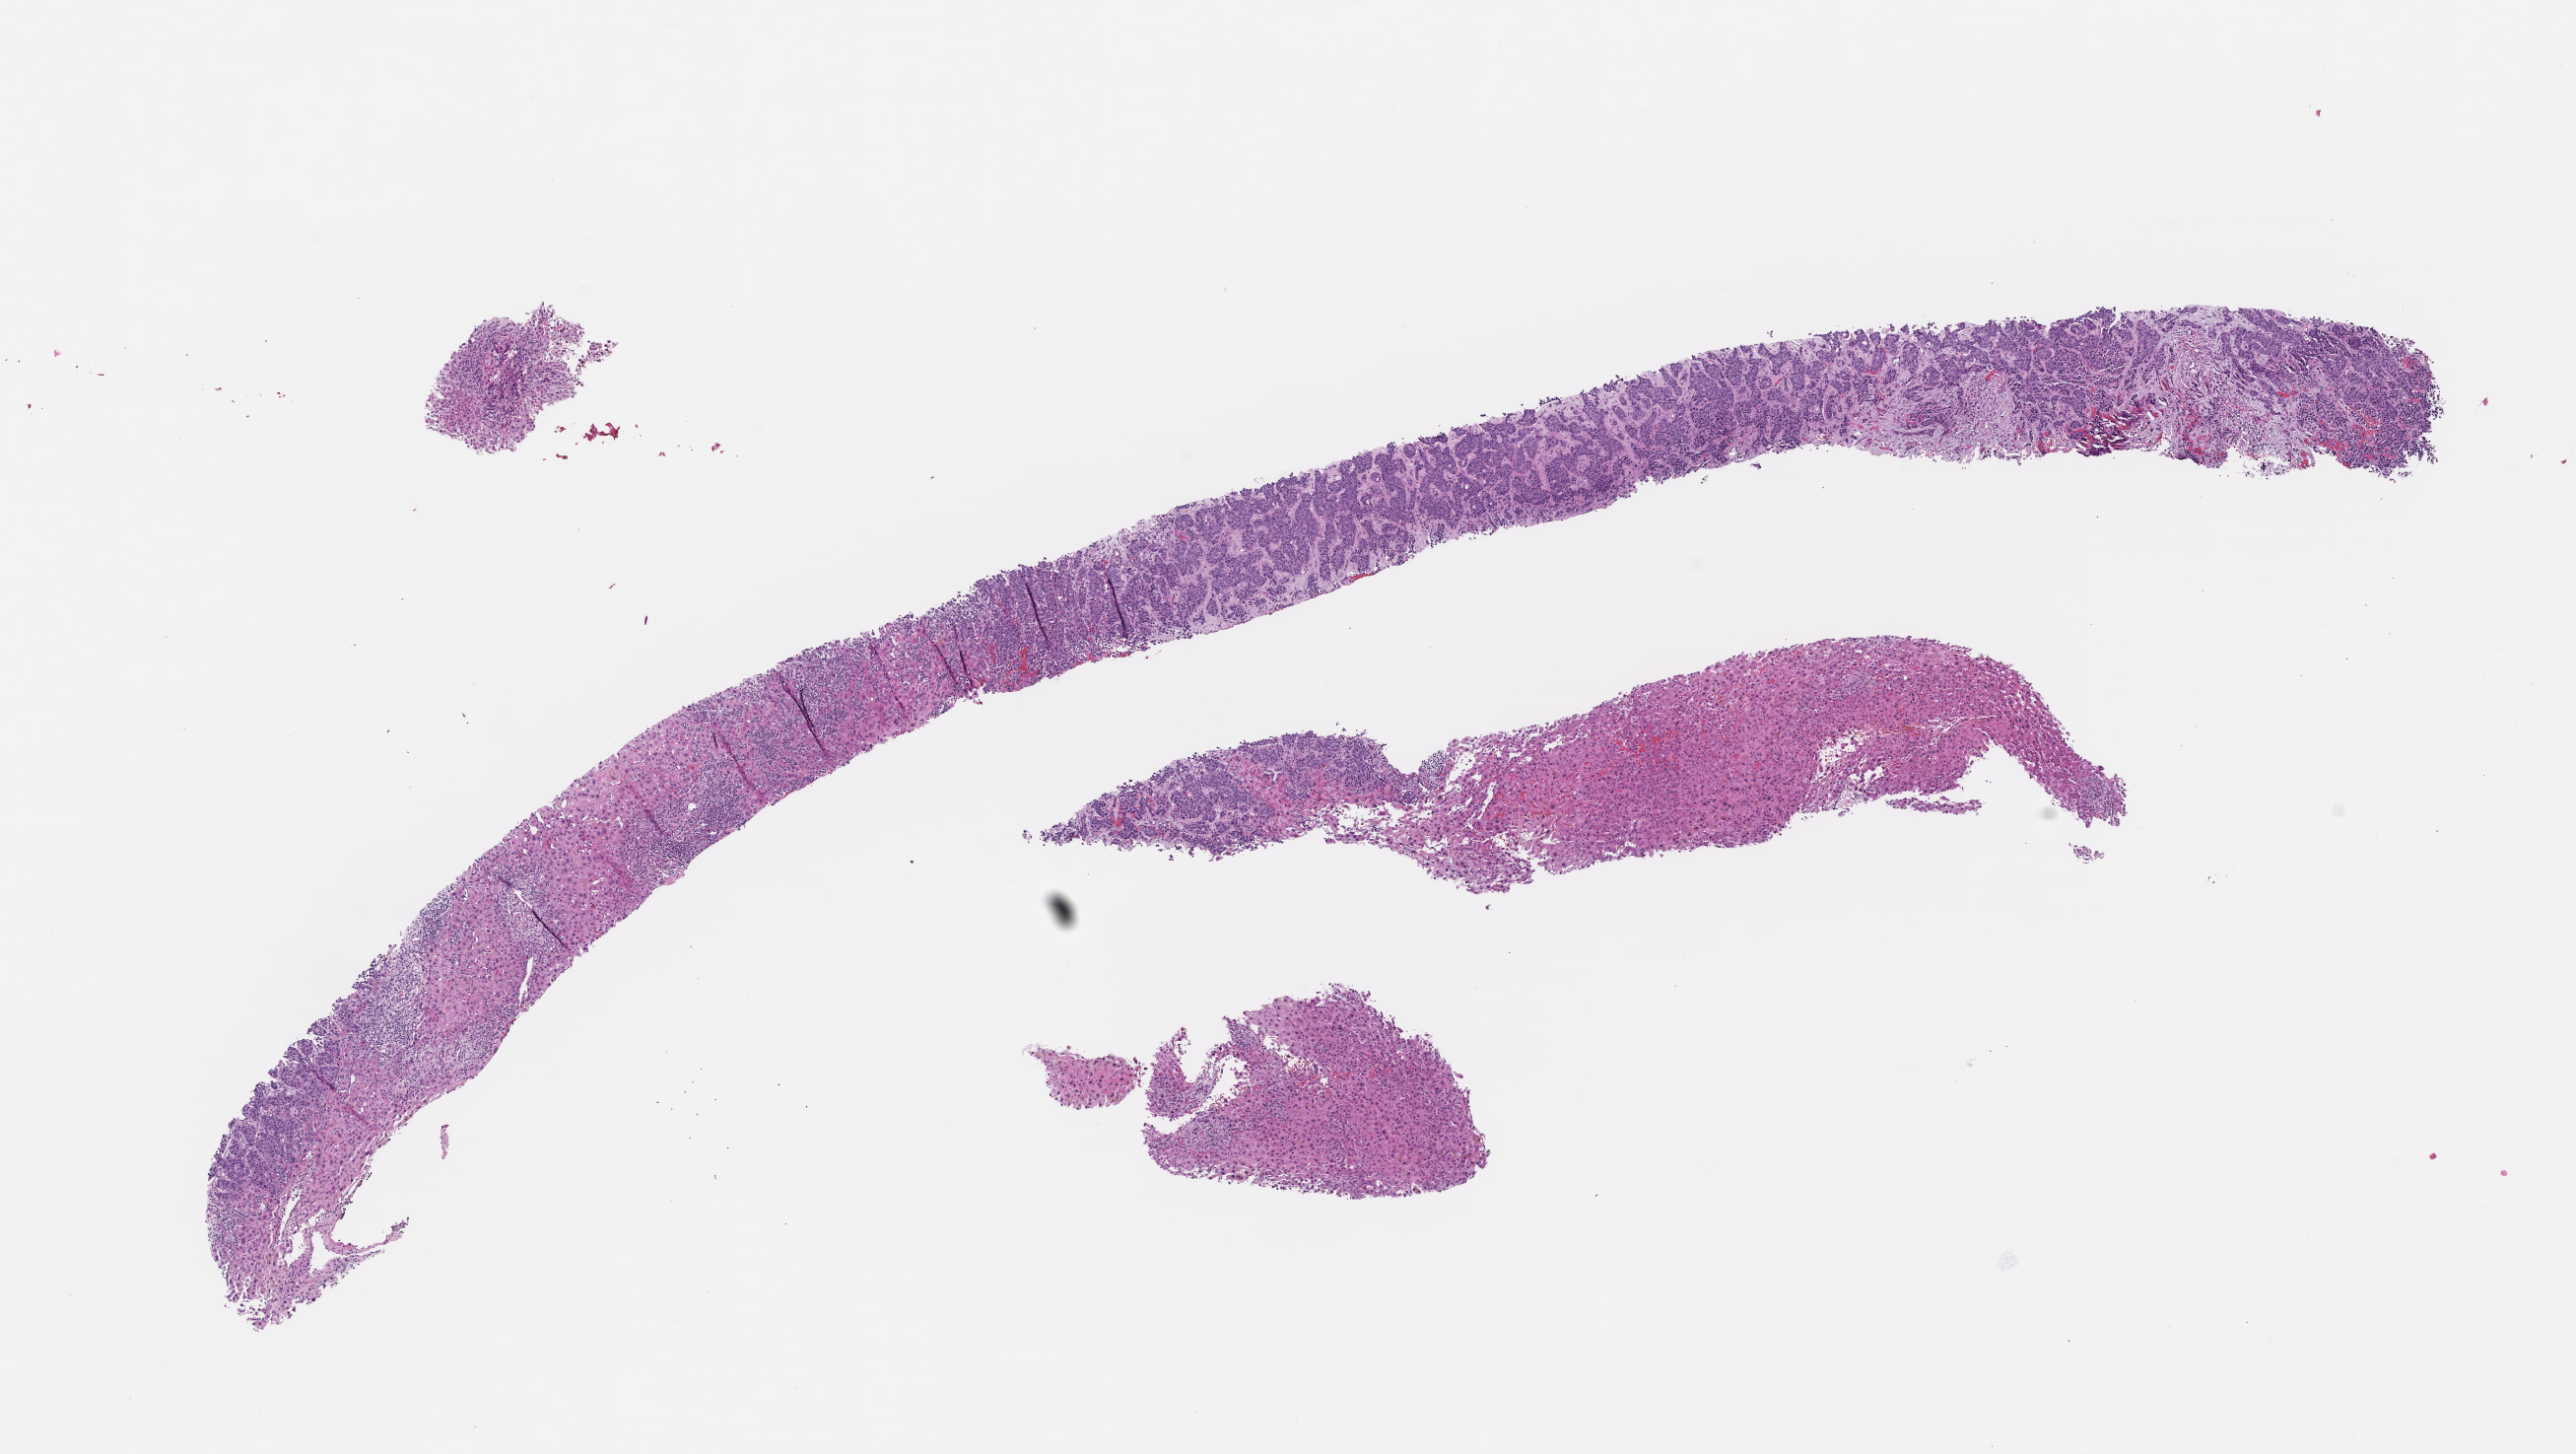
Haematoxylin and eosin whole-slide image, a low-resolution overview of the entire scanned area, about 10.6 x 6.0 mm; formalin-fixed paraffin-embedded section; archival tissue. Patient sex: female.
This section: metastasis (sampled organ not recorded). Patient diagnosis (primary): Invasive Breast Carcinoma.